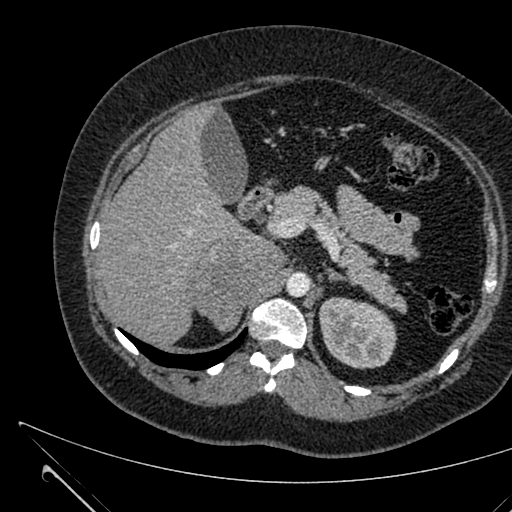
Contrast-enhanced abdominal CT, one axial slice; position 429 of 731 along the scan axis; intravenous contrast given; soft-tissue window (W 400 / L 40 HU); 512 × 512 image matrix. Female patient, age 36 years. Case-level facts recorded for this patient, not image findings: diagnosis: adrenocortical carcinoma; tumour side: right adrenal.
Outlined on this slice (semi-automatically segmented with operator editing):
- mass: bounding box <188,236,283,331> (left, top, right, bottom; pixels)